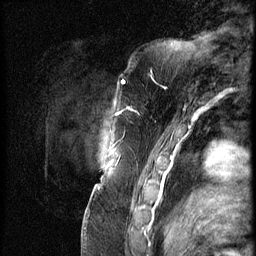
Breast MRI (dynamic contrast-enhanced), one sagittal slice; position 9 of 62 along the scan axis; 3 images stored at this slice position (order not interpretable as contrast timing); 1.5 T; TE 4.2 ms, TR 9 ms; 256 × 256 image matrix, field of view 180 × 180 mm. Patient: female, 57 years. Case-level facts recorded for this patient, not image findings: setting: breast cancer imaged before/during neoadjuvant chemotherapy; receptor status: triple-negative.
Outlined on this slice (semi-automatically segmented with operator editing):
- analysis volume of interest (the breast-tissue region the enhancement analysis was run in; not a lesion): bounding box <105,84,158,135> (left, top, right, bottom; pixels)
- tumour enhancement mask (voxels above the 140 % enhancement threshold inside the analysis volume of interest): <117,108,136,115>